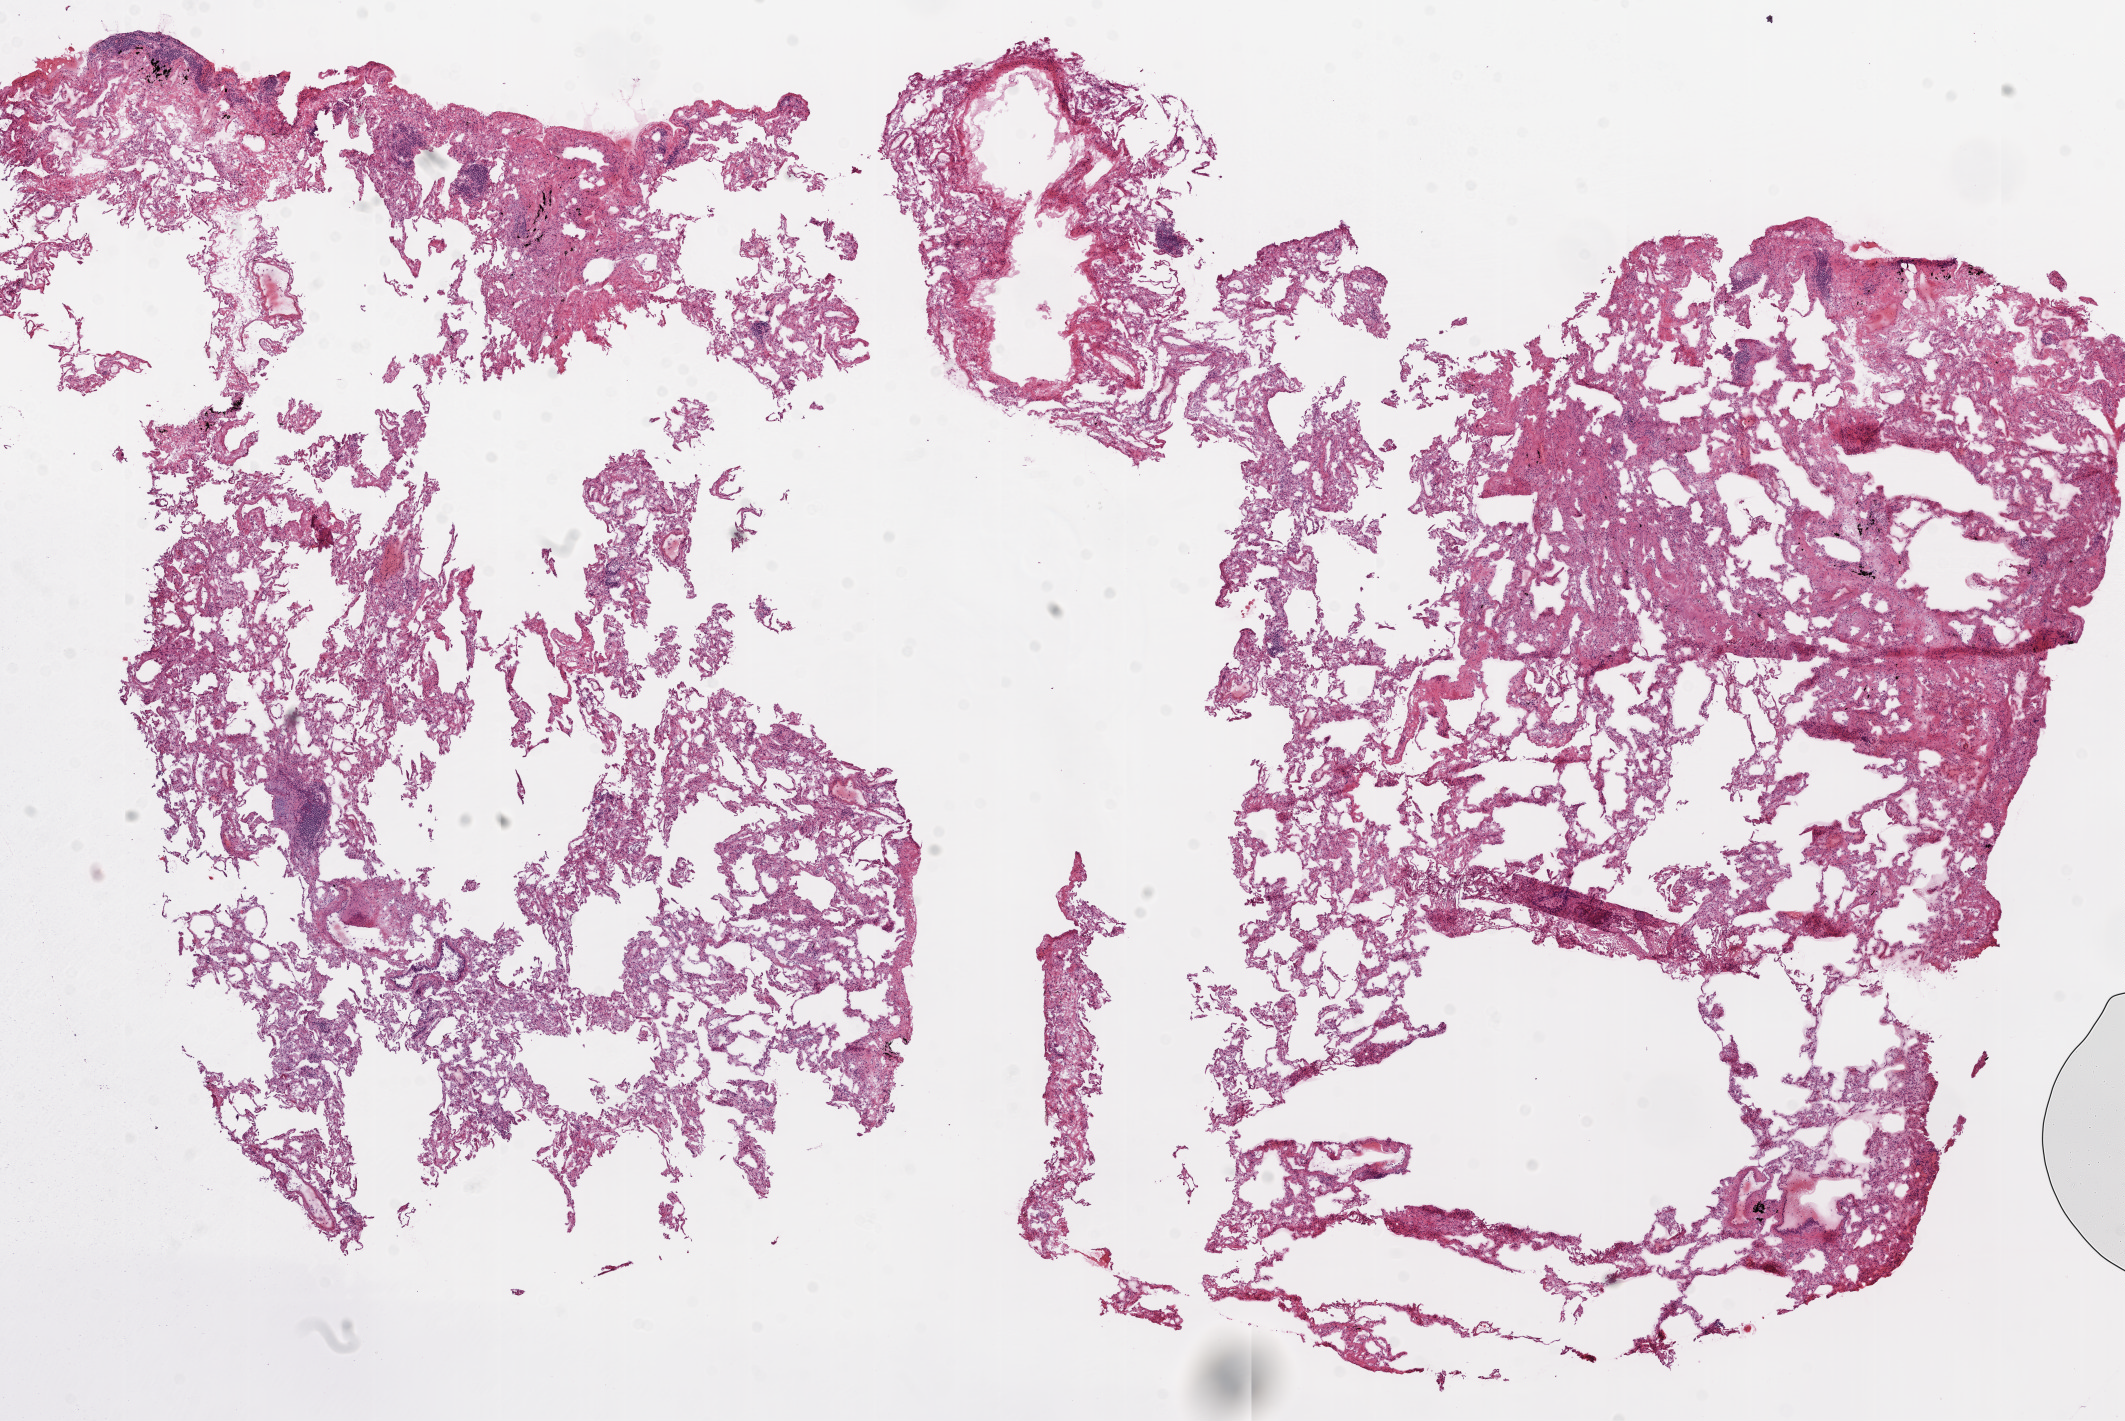
Digitized H&E tissue section (whole slide), whole scanned area (about 17.1 x 11.4 mm, slide scanned at 20x) shown as a low-resolution overview; frozen section from the bottom of the tissue portion; sample: solid tissue normal (non-tumour tissue), lung. Female, age 76 years at initial diagnosis.
This section: solid tissue normal (non-tumour) sample from the same patient. Patient diagnosis: Squamous cell carcinoma, NOS.